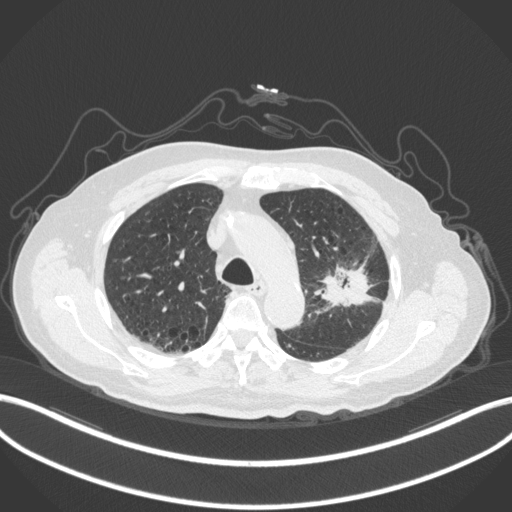
Chest CT, one axial slice; position 216 of 331 along the scan axis; reconstruction kernel B31f; 120 kVp; lung window (W 1500 / L -600 HU); 1 mm slice thickness; 512 × 512 image matrix. Male patient, age 79 years. Case-level facts recorded for this patient, not image findings: clinical TNM (as recorded): T2a N1 M1; histopathological grade: G3.
Structures marked on this image (rectangle marked by the reading radiologist):
- lung tumour (recorded histology: adenocarcinoma): box from (x=321, y=264) to (x=376, y=310) px